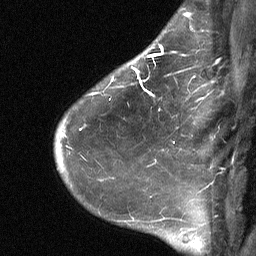
Breast MRI (dynamic contrast-enhanced), one sagittal slice. Position 49 of 64 along the scan axis. Dynamic contrast-enhanced study with each time point stored as its own series, time point 2 of 3 at this slice position (early post-contrast, ordered by acquisition time). 1.5 T. TE 4.8 ms, TR 27 ms. 256 × 256 image matrix, field of view 180 × 180 mm. Female patient, age 51 years. From the clinical record (not read from this slice): setting: breast cancer imaged before/during neoadjuvant chemotherapy; receptor status: HR-positive, HER2-negative.
Structures marked on this image (semi-automatically segmented with operator editing):
- analysis volume of interest (the breast-tissue region the enhancement analysis was run in; not a lesion): bounding box <72,34,182,118> (left, top, right, bottom; pixels)
- tumour enhancement mask (voxels above the 90 % enhancement threshold inside the analysis volume of interest): <112,44,177,96>